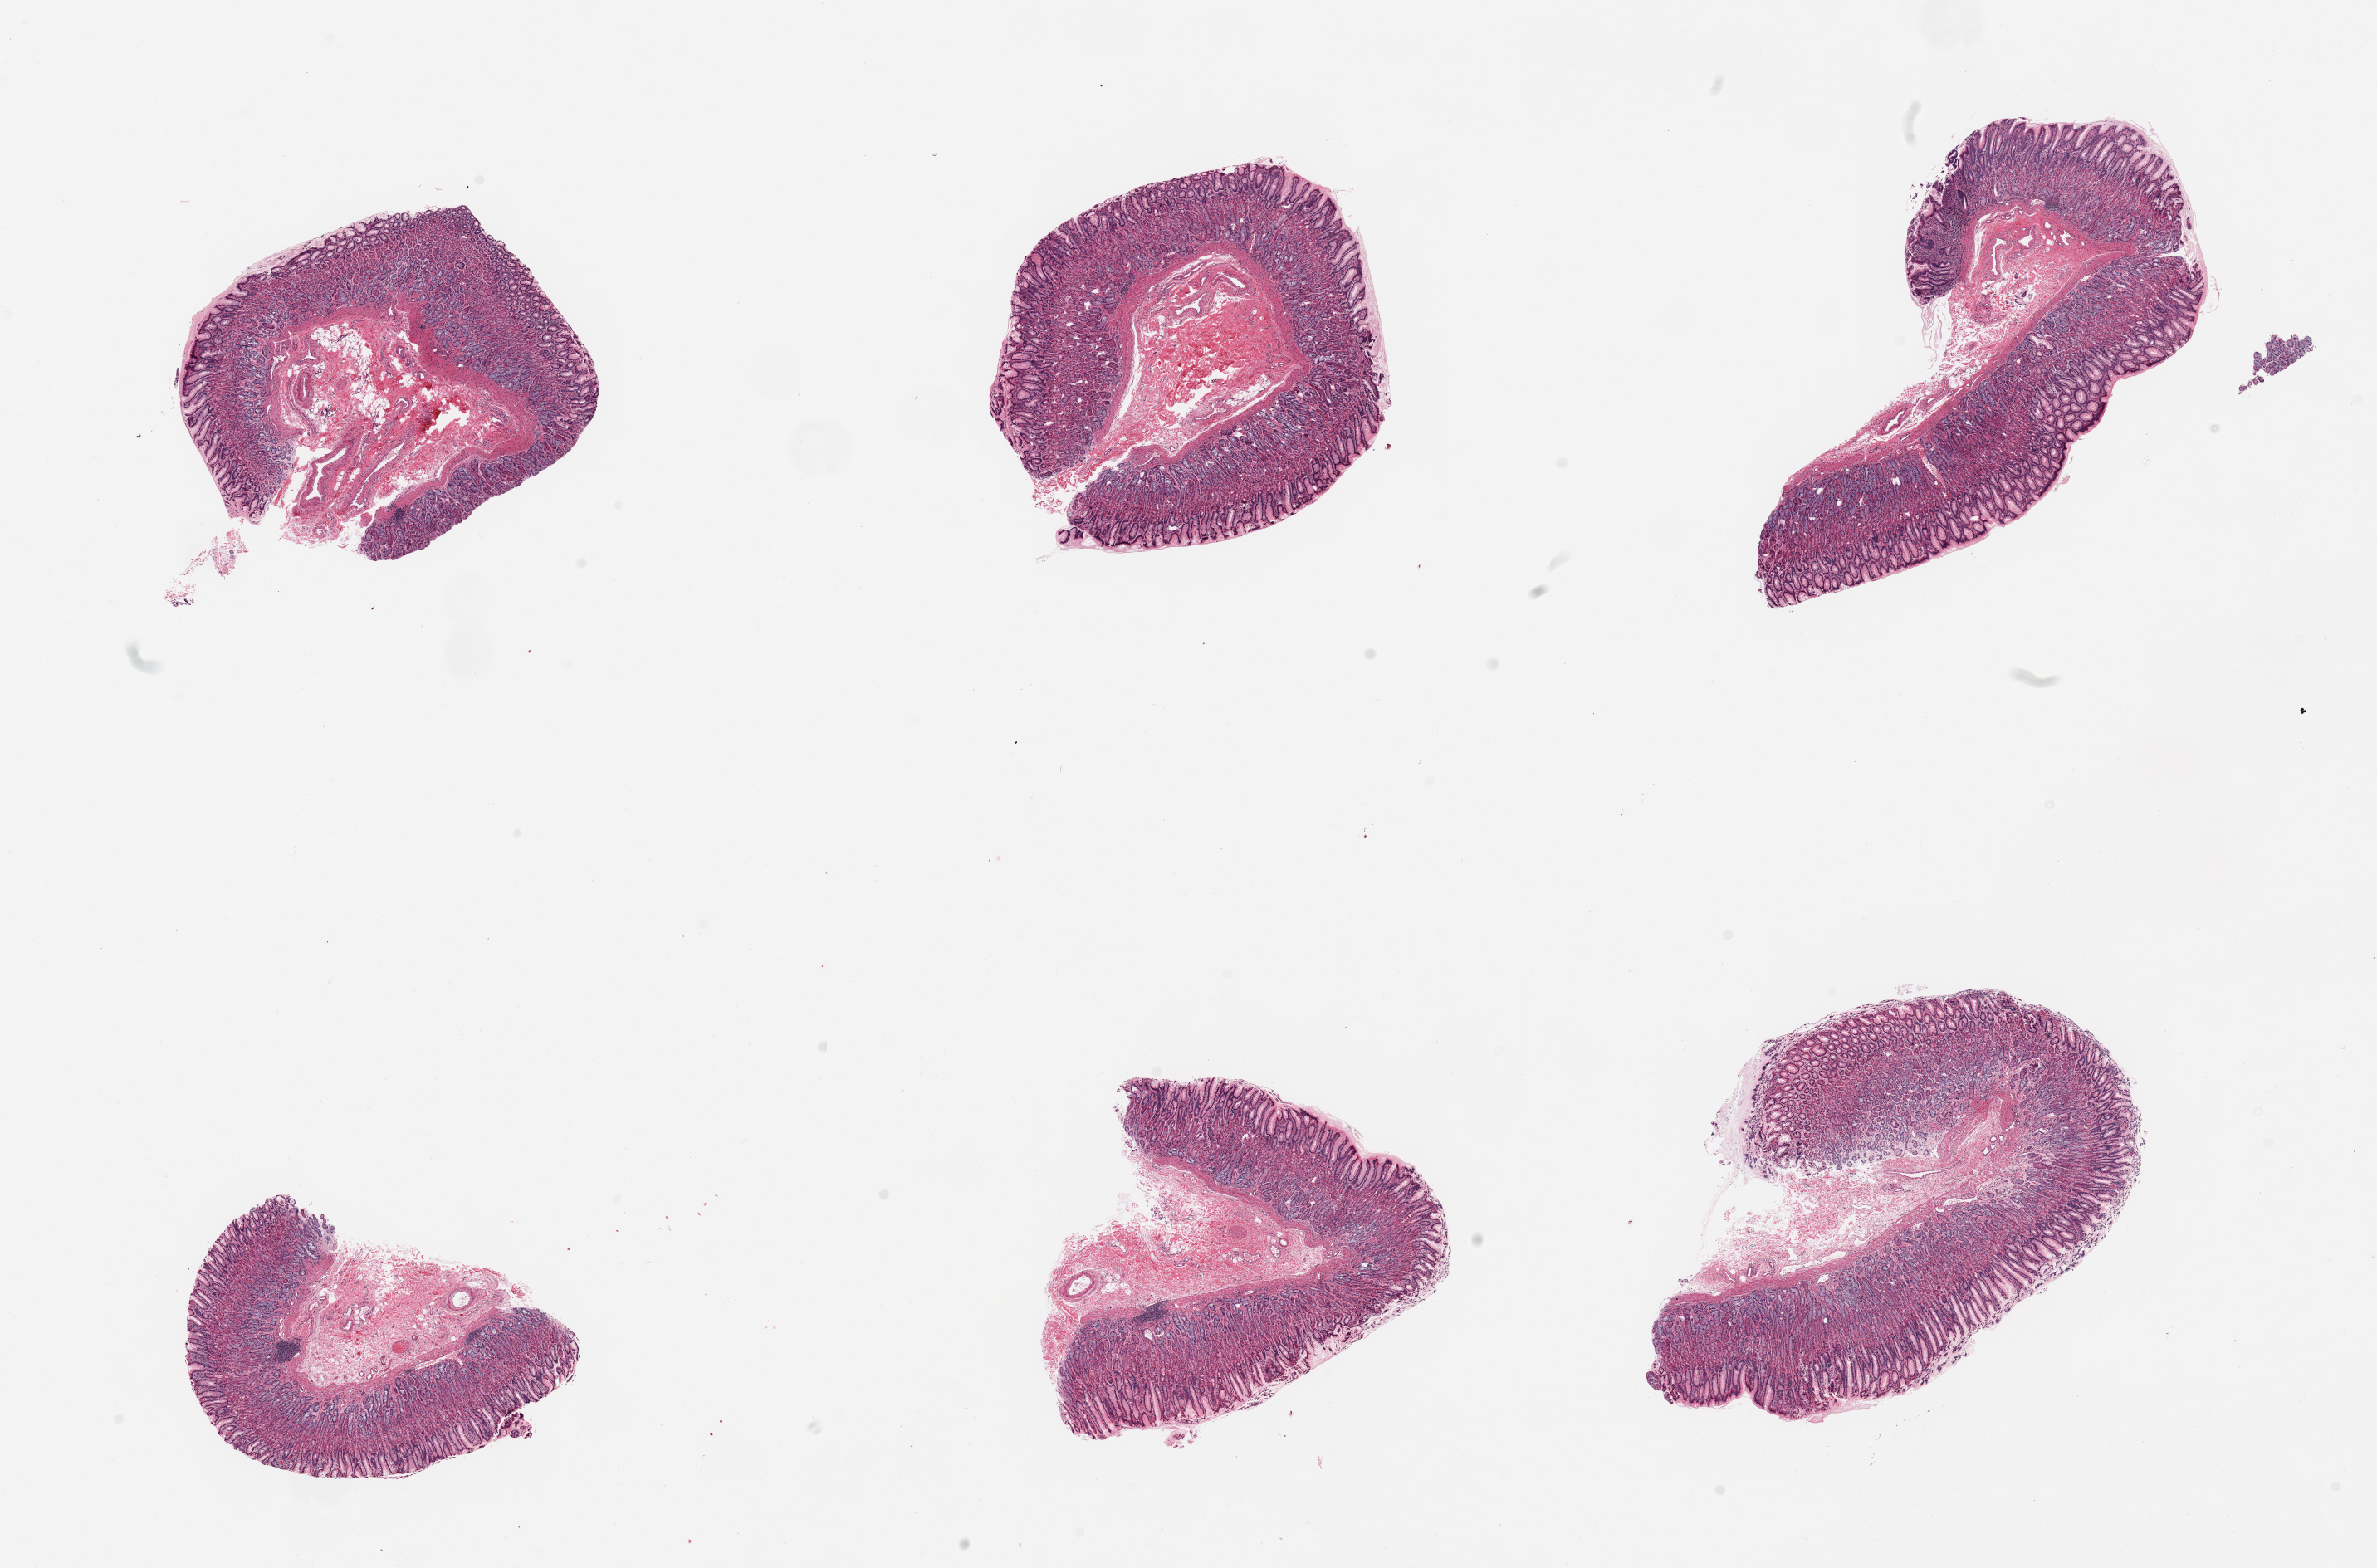
Hematoxylin and eosin (H&E) whole-slide image, brightfield — low-resolution overview of the scanned area, about 22.6 x 14.9 mm (from a 20x scan). PAXgene-fixed, paraffin-embedded tissue. Target tissue: stomach. Donor tissue sample. Donor: male.
* pathologist's review note for this sample: 6 pieces; mucosa and submucosa only, no muscularis